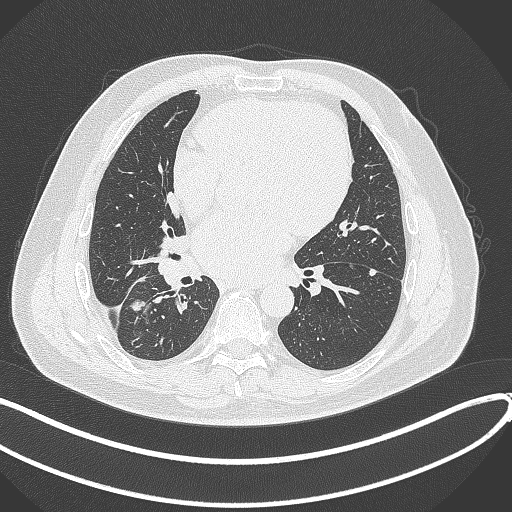
Chest CT, one axial slice; position 170 of 360 along the scan axis; reconstruction kernel B70f; 120 kVp; lung window (W 1500 / L -600 HU); 1 mm slice thickness; 512 × 512 image matrix, field of view 400 × 400 mm. Patient: male, 59 years.
Outlined on this slice (rectangle marked by the reading radiologist):
- lung tumour (recorded histology: adenocarcinoma): bounding box (x1, y1, x2, y2) in pixels: (131, 294, 152, 319)